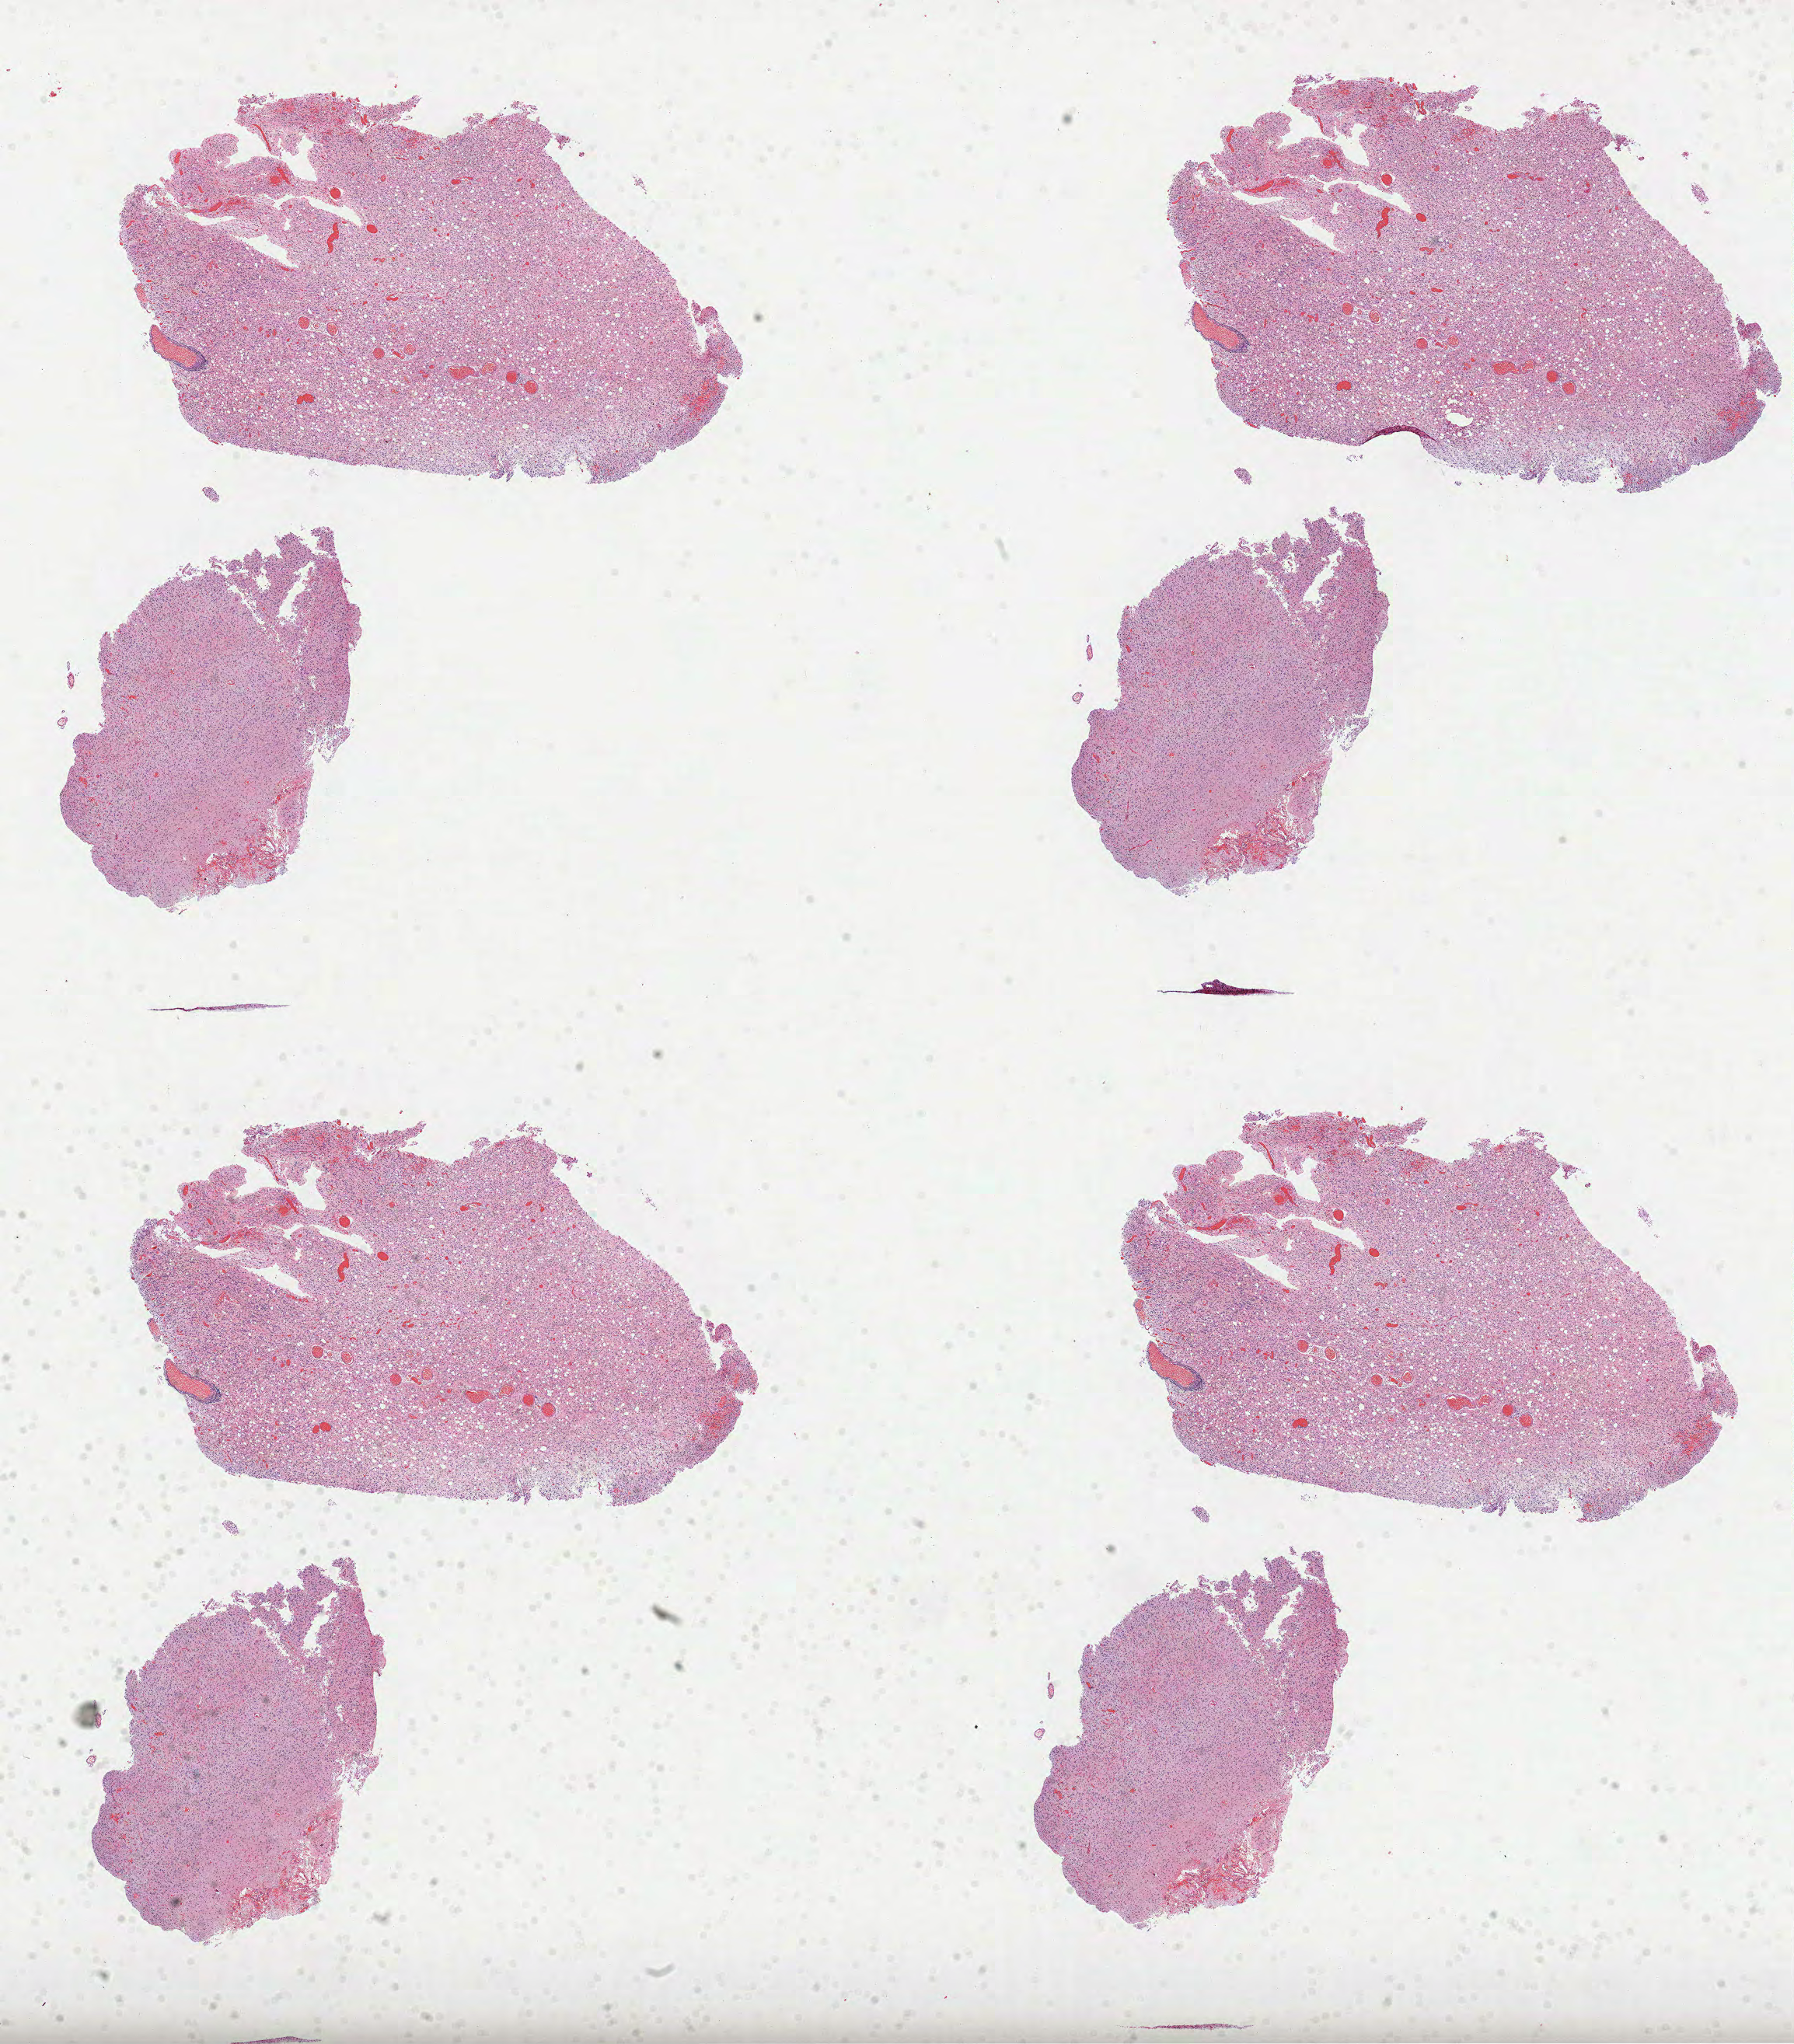
Whole-slide histology image, H&E, whole scanned area (about 18.6 x 21.2 mm, acquisition: 40x scan) shown as a low-resolution overview; FFPE section; primary tumour sample from the brain. Patient: male, age at initial diagnosis 48 years. Histologic grade: G2 (moderately differentiated).
- laterality: left
- diagnosis: Oligodendroglioma, NOS